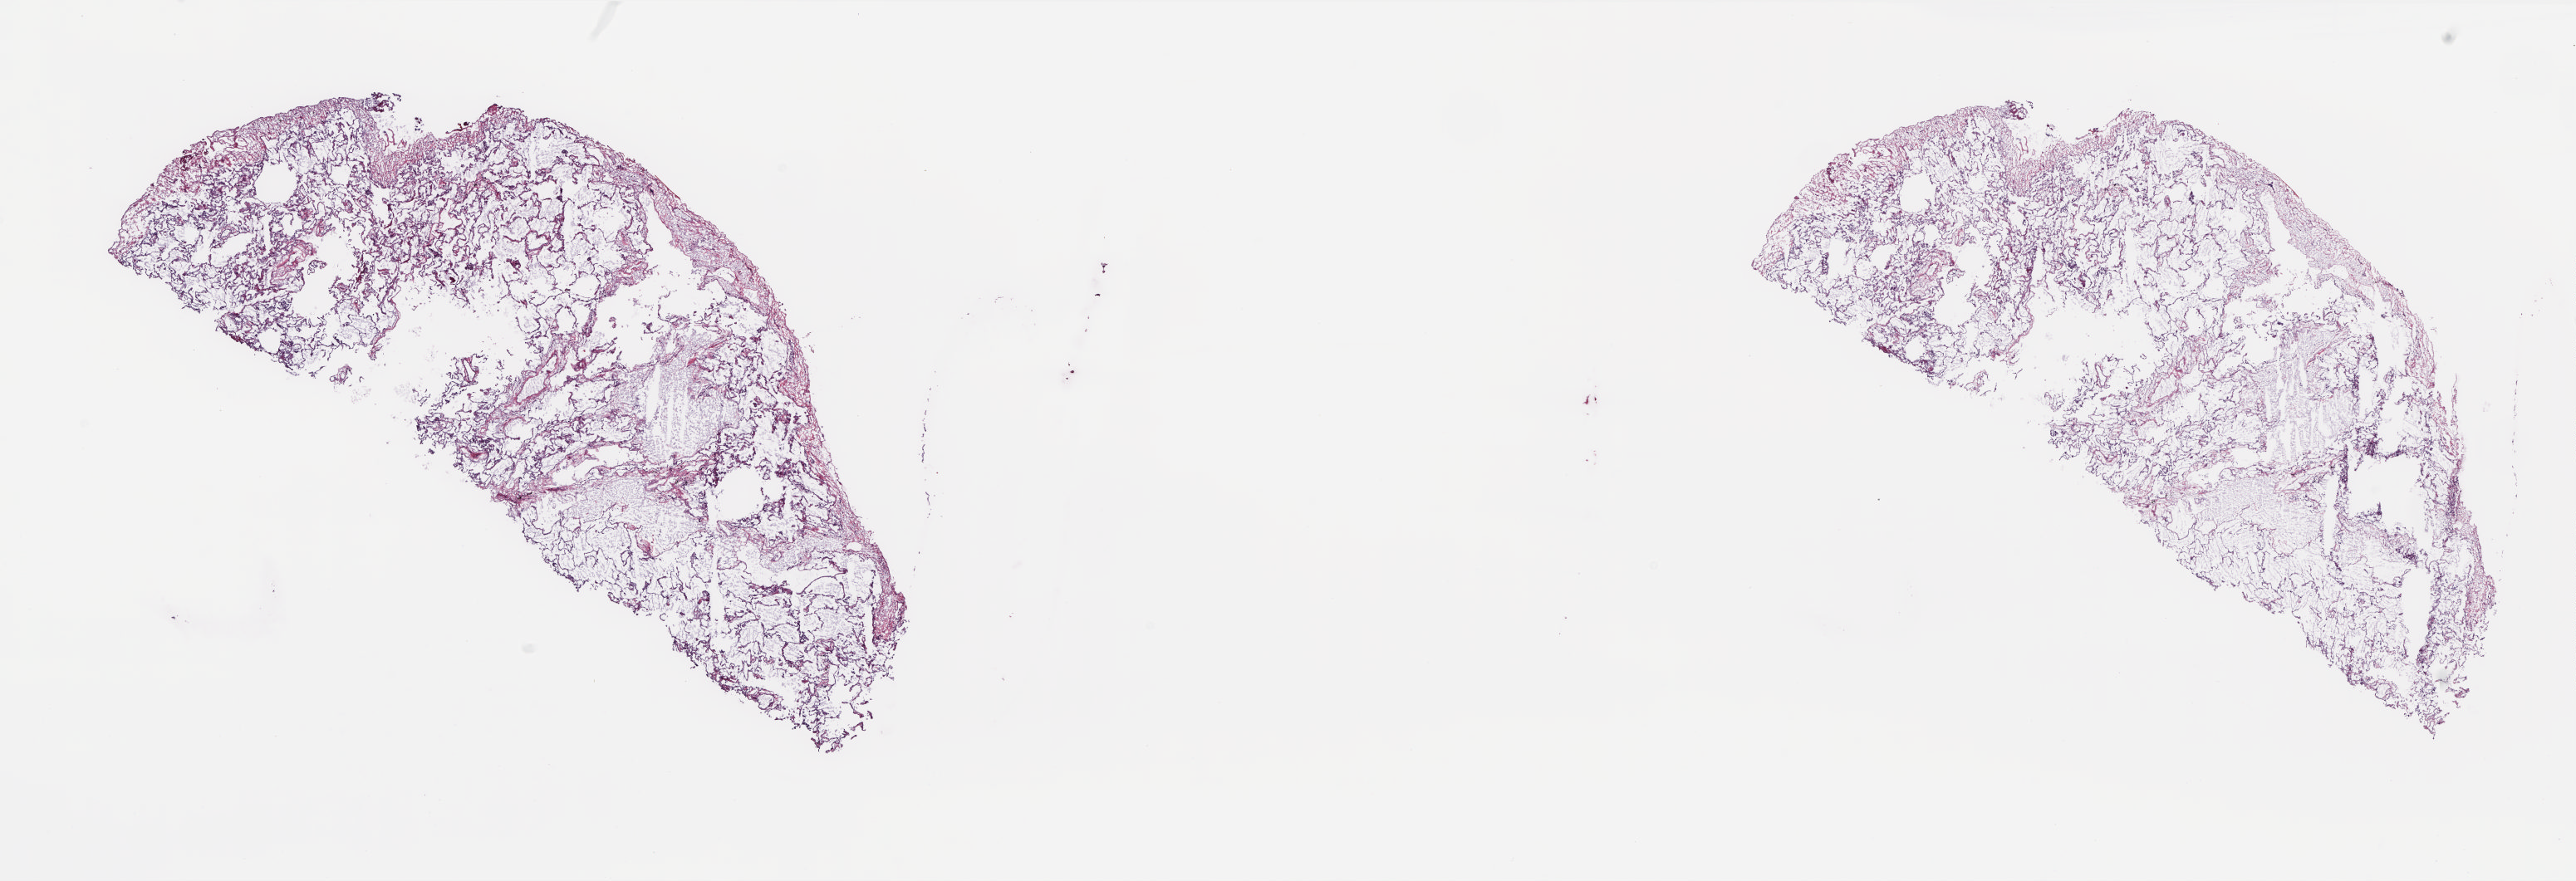
Digitized Hematoxylin and eosin (H&E) stained tissue section (whole slide), shown as a low-resolution overview of the whole scanned area (about 25.0 x 8.6 mm); frozen section from the top of the tissue portion; sample: solid tissue normal (non-tumour tissue), lung. Female, age 72 years at initial diagnosis. Slide review estimates, as recorded: tumour cells 0%, tumour nuclei 0%.
This section: solid tissue normal (non-tumour) sample from the same patient. Patient diagnosis: Adenocarcinoma, NOS (upper lobe, lung).